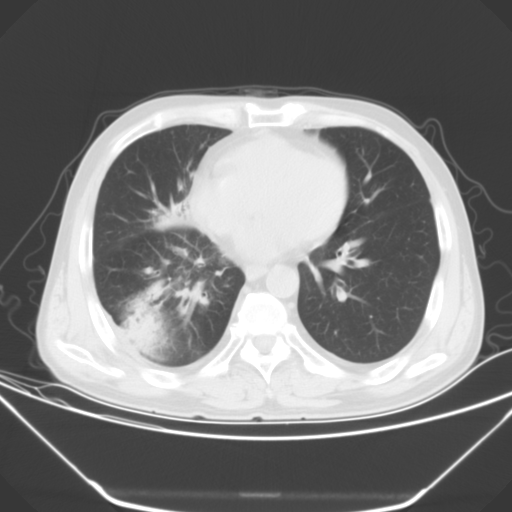
Chest CT, one axial slice. Position 19 of 52 along the scan axis. 120 kVp. Lung window (W 1500 / L -600 HU). 5 mm slice thickness. 512 × 512 image matrix, field of view 379 × 379 mm. Male patient, age 54 years. From the clinical record (not read from this slice): clinical TNM (as recorded): T2 N1 M0.
Annotated regions visible in this slice (bounding box drawn by a radiologist):
- lung tumour (recorded histology: adenocarcinoma): bounding box [x1, y1, x2, y2] px = [125, 283, 162, 352]